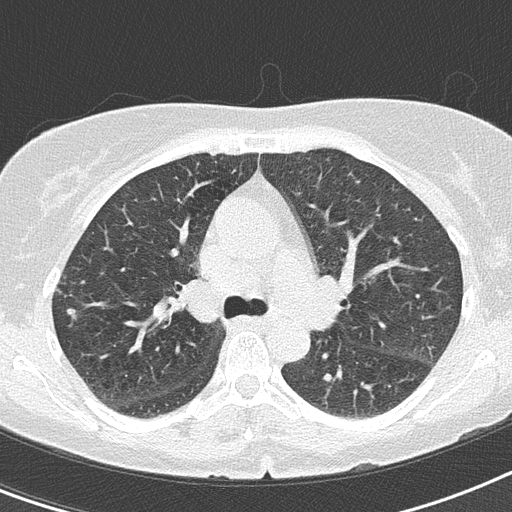
Axial slice from a low-dose chest CT screening exam; second screening round (one year after baseline); lung window (W 1500 / L -600 HU); lung (sharp) reconstruction kernel (B50f); slice 57 of 147 in the series. Female, age 61 years at enrolment.
Expert reader's lesion annotation, bounding box [x1, y1, x2, y2] px = [47, 296, 94, 339]. Screening reader's record for this exam: no non-calcified nodule ≥4 mm recorded. Official screen result: negative screen, significant abnormalities not suspicious for lung cancer. Participant outcome: lung cancer diagnosed 125 days after this screen — small cell carcinoma, NOS, right upper lobe, stage IIIA (AJCC 6th edition), 7 mm at pathology.